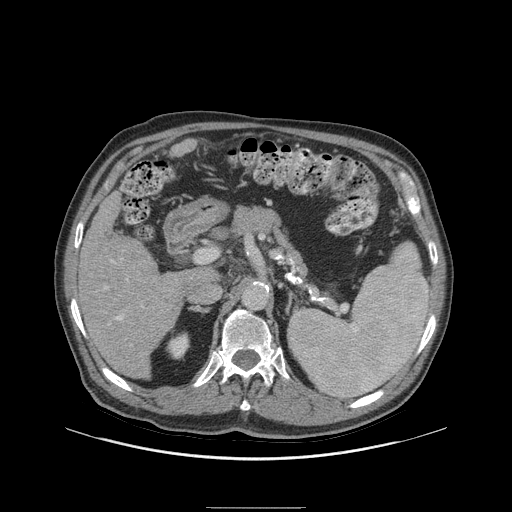
Contrast-enhanced abdominal CT (liver protocol), one axial slice; slice 50 of 105 in the series (ordered by position); 140 kVp; soft-tissue window (W 400 / L 40 HU); 2.5 mm slice thickness; 512 × 512 image matrix. Case-level facts recorded for this patient, not image findings: diagnosis: hepatocellular carcinoma (patient treated with transarterial chemoembolisation; whether this scan precedes or follows treatment is not stated here); TNM stage (as recorded): Stage-I; Child-Pugh class: A.
Structures marked on this image (semi-automatic segmentation, software-assisted and operator-edited):
- liver parenchyma outside the tumour (the mass and vessels are separate outlines, so this box may not span the whole liver): box from (x=76, y=192) to (x=190, y=378) px
- liver vessels: (x=105, y=260)–(x=123, y=320)